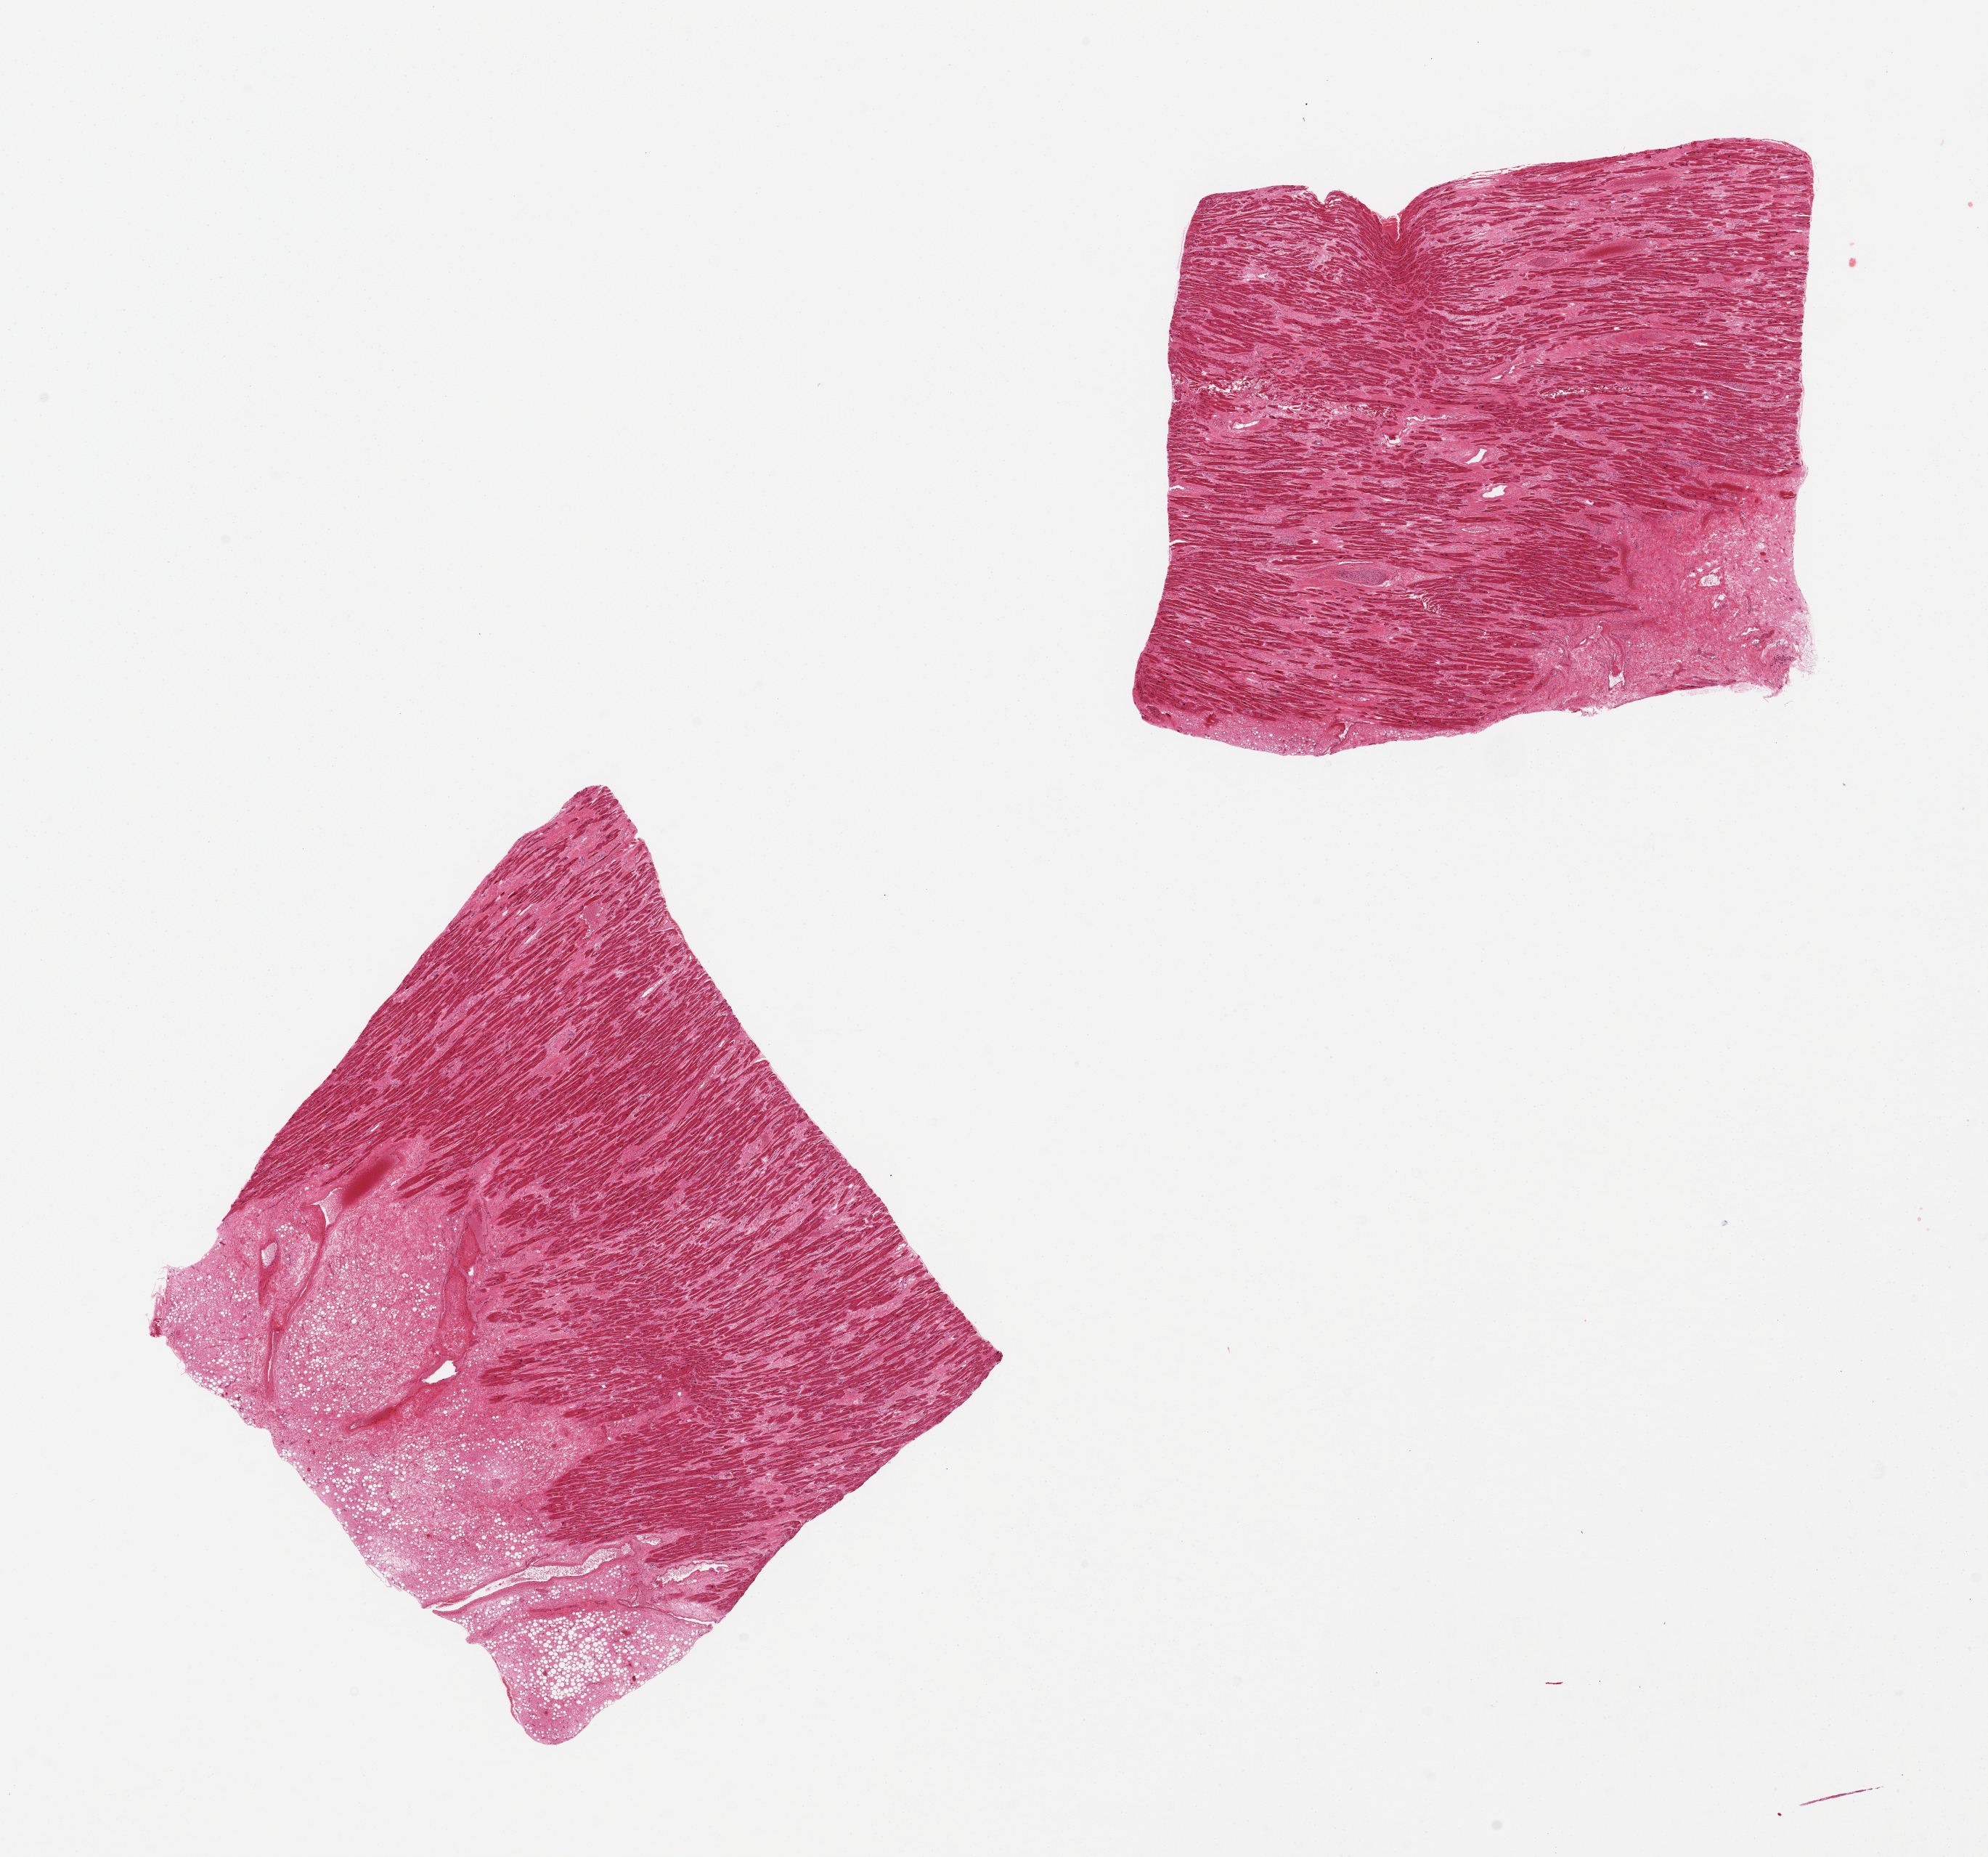
Whole-slide image, H&E stain, brightfield, low-resolution overview of the scanned area, about 21.7 x 20.2 mm (from a 20x scan). PAXgene-fixed, paraffin-embedded tissue. Target tissue: heart. Tissue donor sample. Donor sex: female.
Reviewer comment on this tissue sample: 2 pieces, extensive chronic/subacute infarcts.